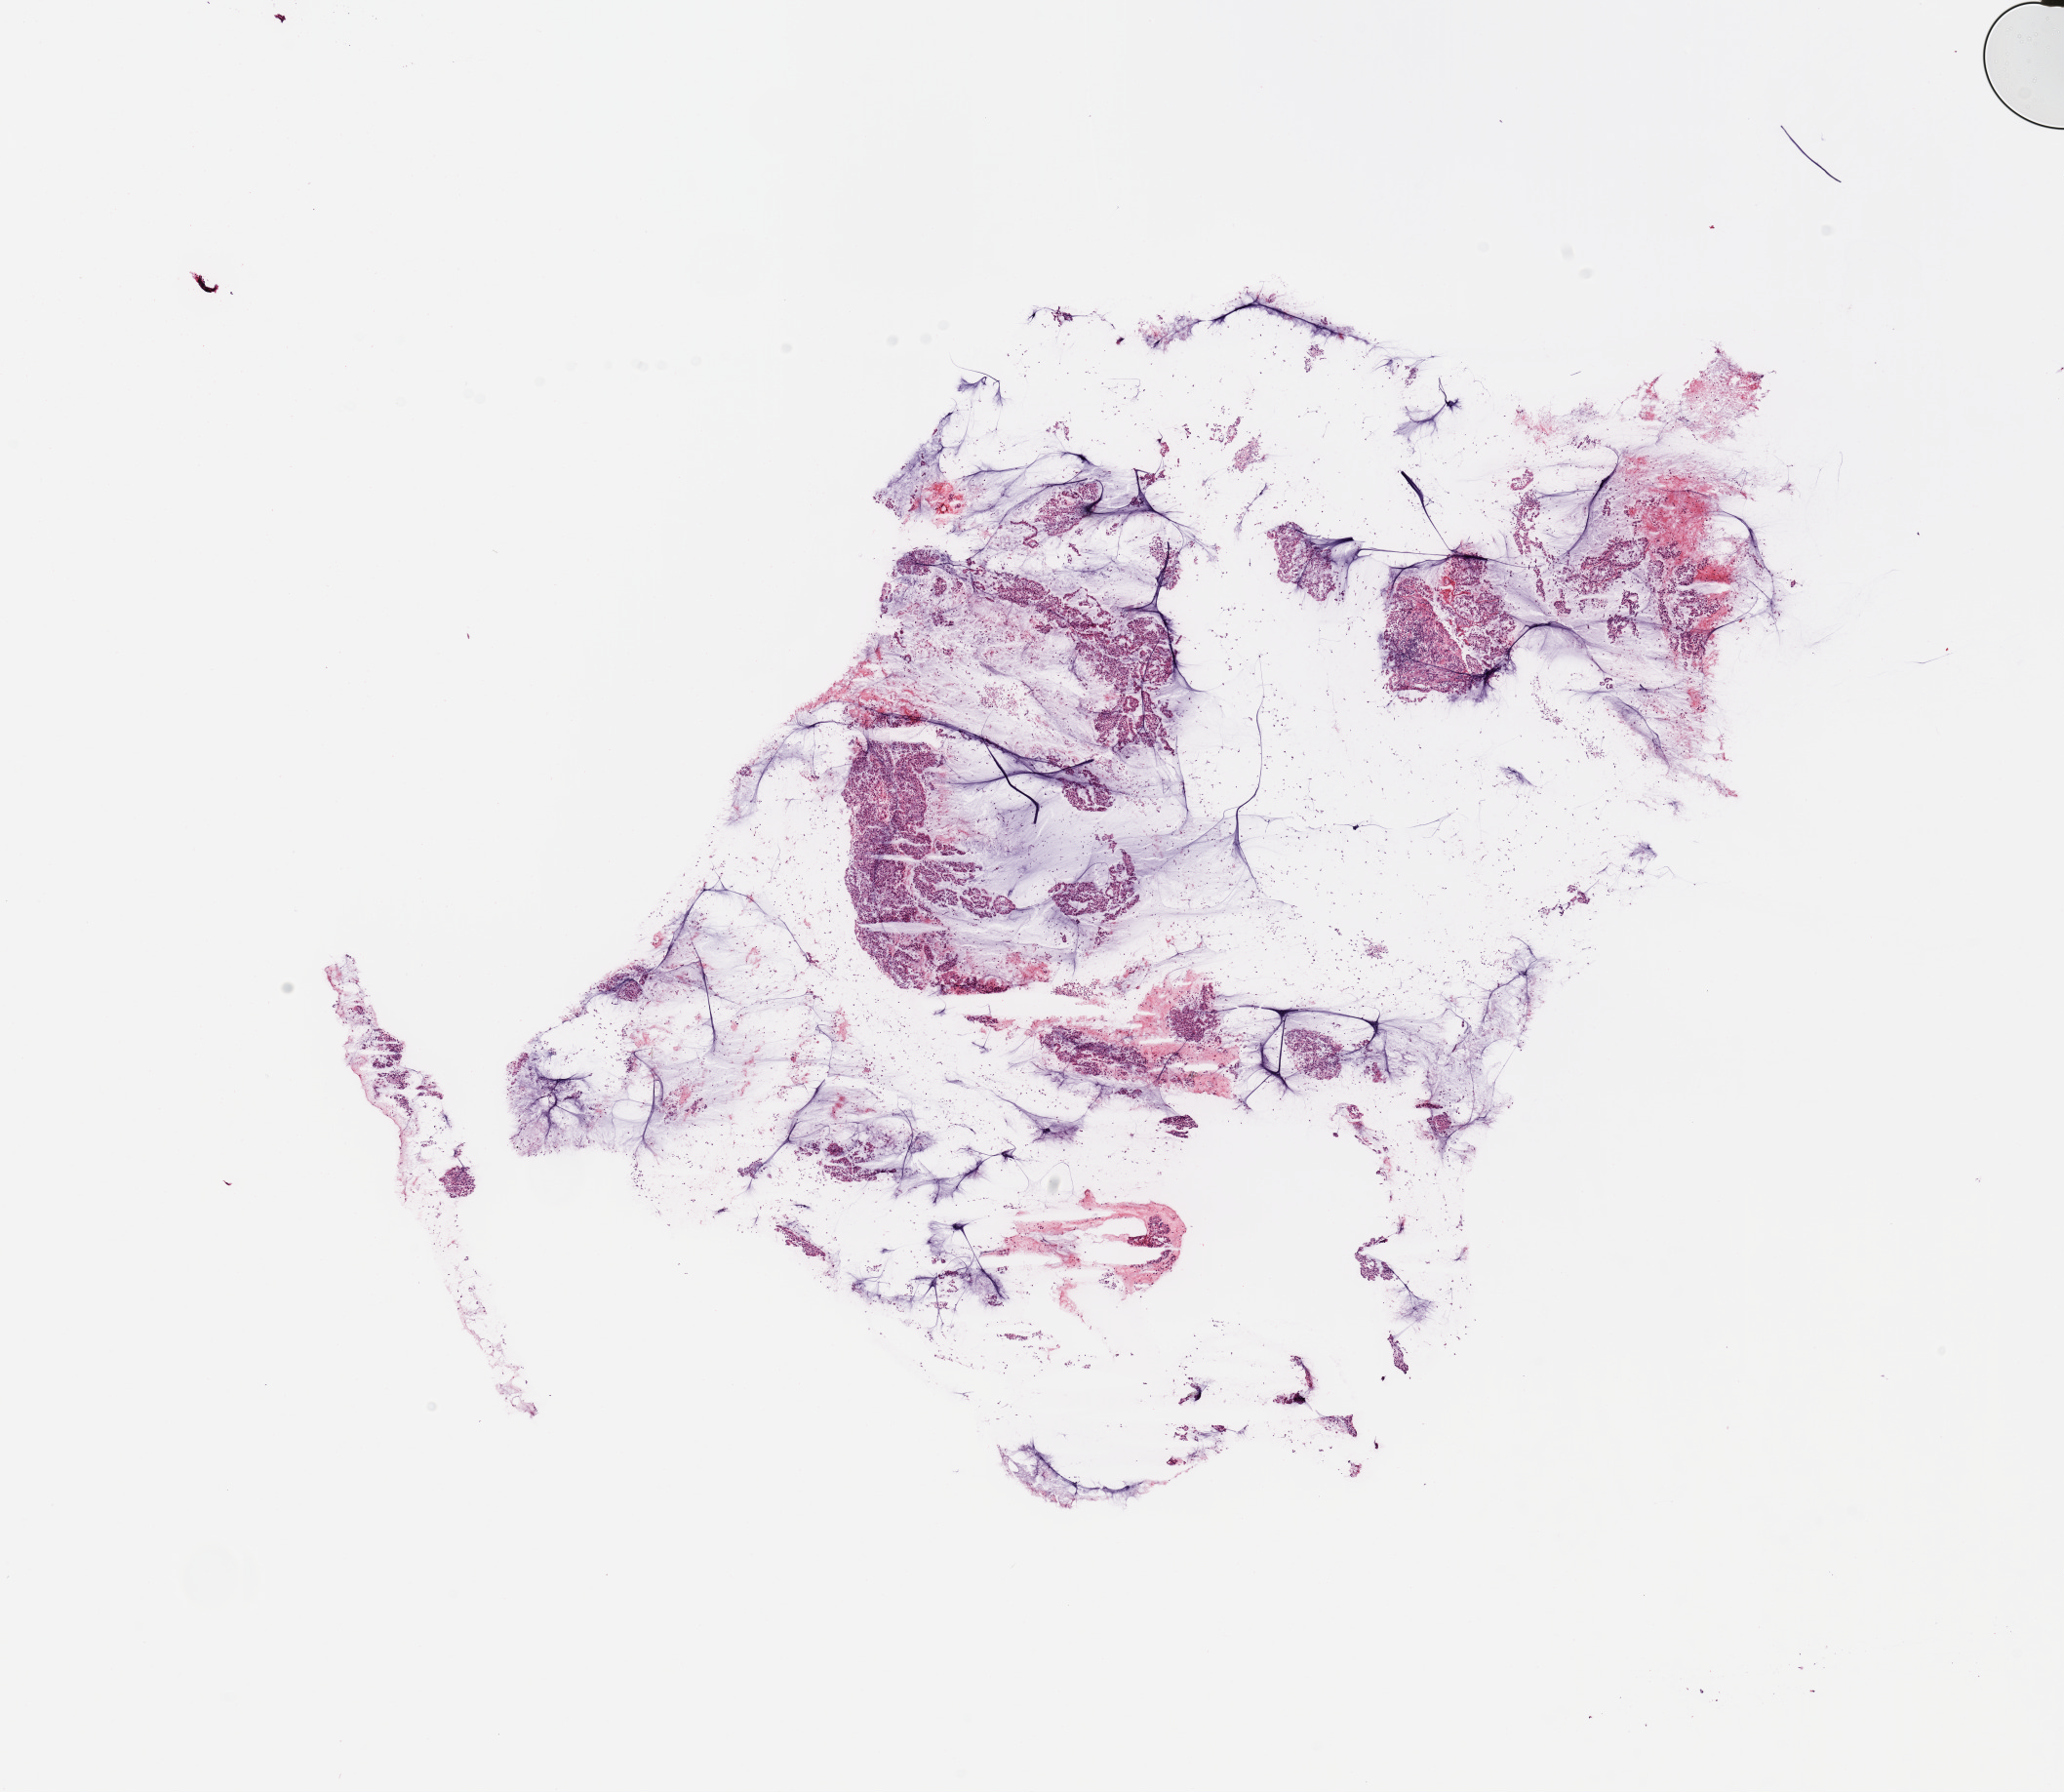
Whole-slide histology image, H&E-stained, low-resolution overview of the scanned area, about 16.7 x 14.5 mm (from a 20x scan). Tumour tissue sample, lung. Female, 35 y/o. Histologic grade: G3 (poorly differentiated).
Primary tumour site (as recorded): left lower lobe. Diagnosis: Adenocarcinoma, NOS. AJCC pathologic stage: IB.